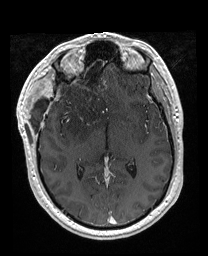
Brain MRI from a brain-tumour surgery series, one axial slice; position 100 of 176 along the scan axis; T1-weighted post-contrast; 1 mm slice thickness; 208 × 256 image matrix, field of view 208 × 256 mm. From the clinical record (not read from this slice): histopathology: Astrocytoma; WHO grade: 4; IDH mutation: yes.
Annotated regions visible in this slice (expert manual segmentation):
- previous resection cavity: bounding box (x1, y1, x2, y2) in pixels: (56, 54, 106, 83)